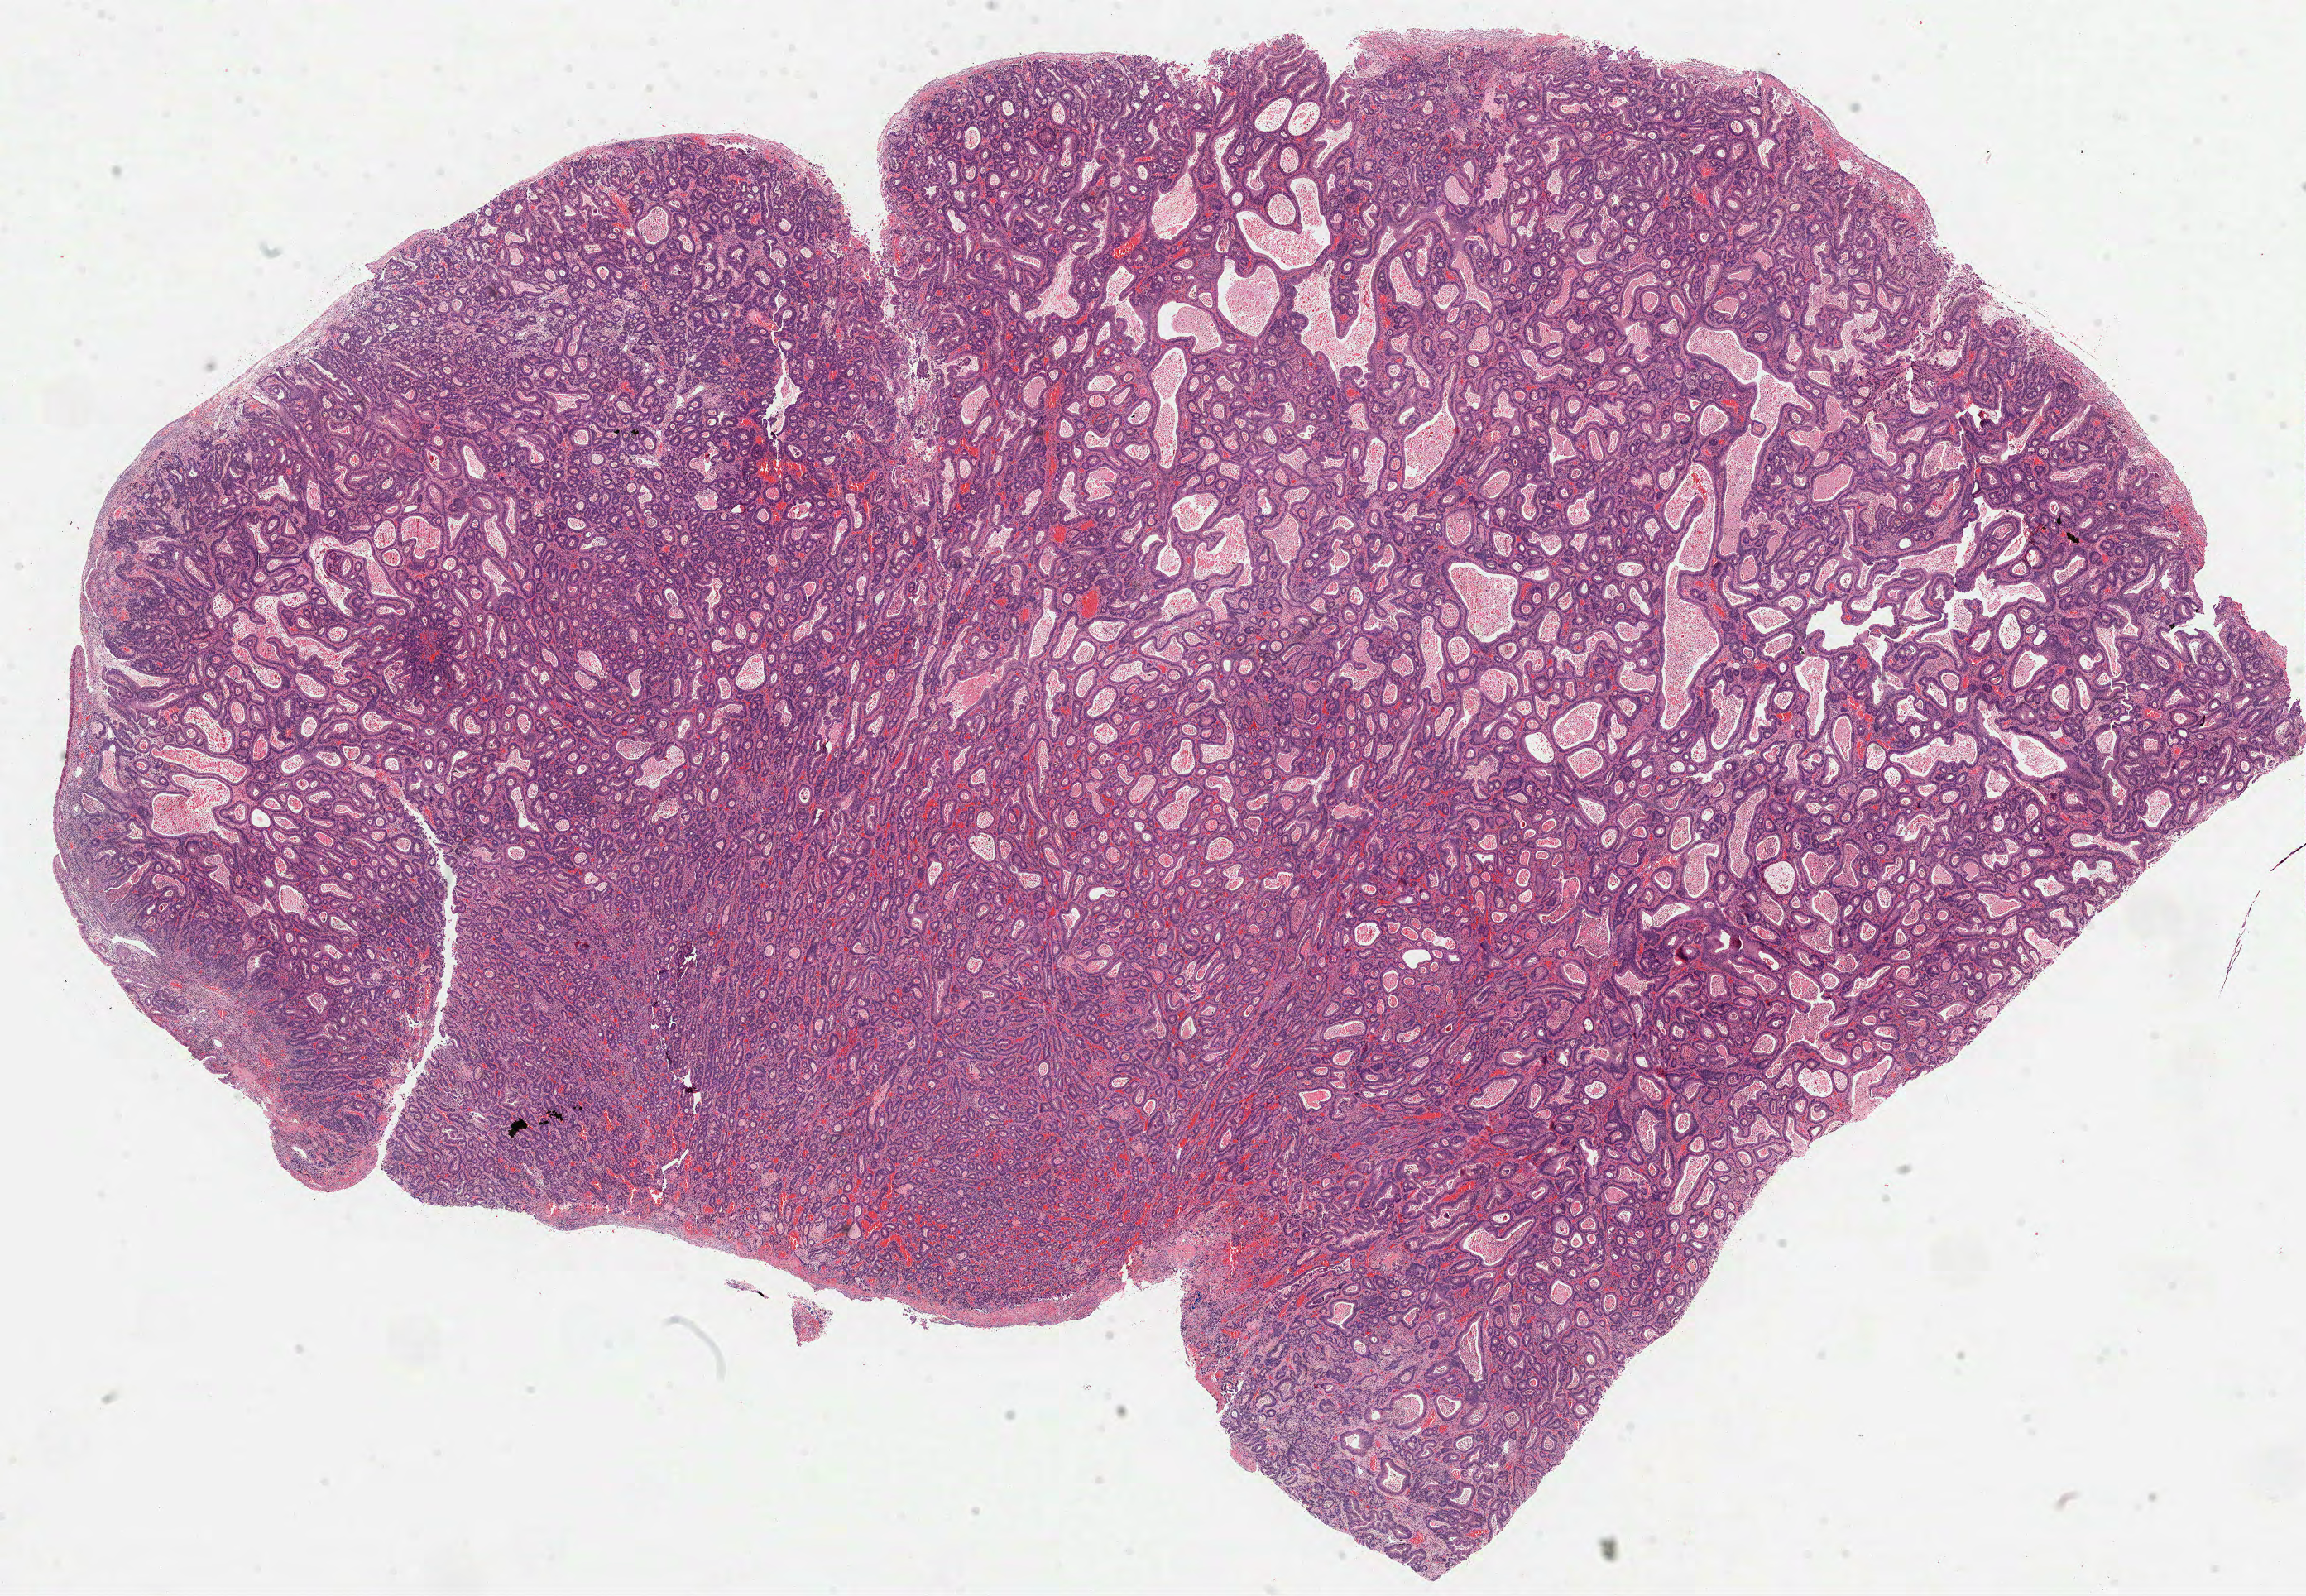
Whole-slide histology image, H&E-stained — low-resolution overview of the scanned area, about 22.5 x 15.6 mm (slide scanned at 40x). Formalin-fixed paraffin-embedded (FFPE) diagnostic section. Stomach, primary tumour sample. Male, age 79 years at initial diagnosis. Histologic grade: G3 (poorly differentiated).
AJCC pathologic stage: IB (7th edition). Histologic diagnosis: Adenocarcinoma, intestinal type (cardia, NOS).